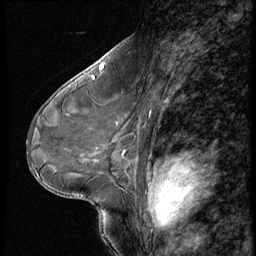
Breast MRI (dynamic contrast-enhanced), one sagittal slice; dynamic contrast-enhanced series, image 2 of 3 at this slice position (ordered by acquisition); 1.5 T; TE 4.2 ms, TR 9 ms; 2.5 mm slice thickness; 256 × 256 image matrix, field of view 180 × 180 mm. Female patient, age 46 years. From the clinical record (not read from this slice): setting: breast cancer imaged before/during neoadjuvant chemotherapy; receptor status: HER2-positive.
Structures marked on this image (semi-automatic segmentation, software-assisted and operator-edited):
- analysis volume of interest (the breast-tissue region the enhancement analysis was run in; not a lesion): bounding box <64,98,174,182> (left, top, right, bottom; pixels)
- tumour enhancement mask (voxels above the 140 % enhancement threshold inside the analysis volume of interest): <155,161,174,182>